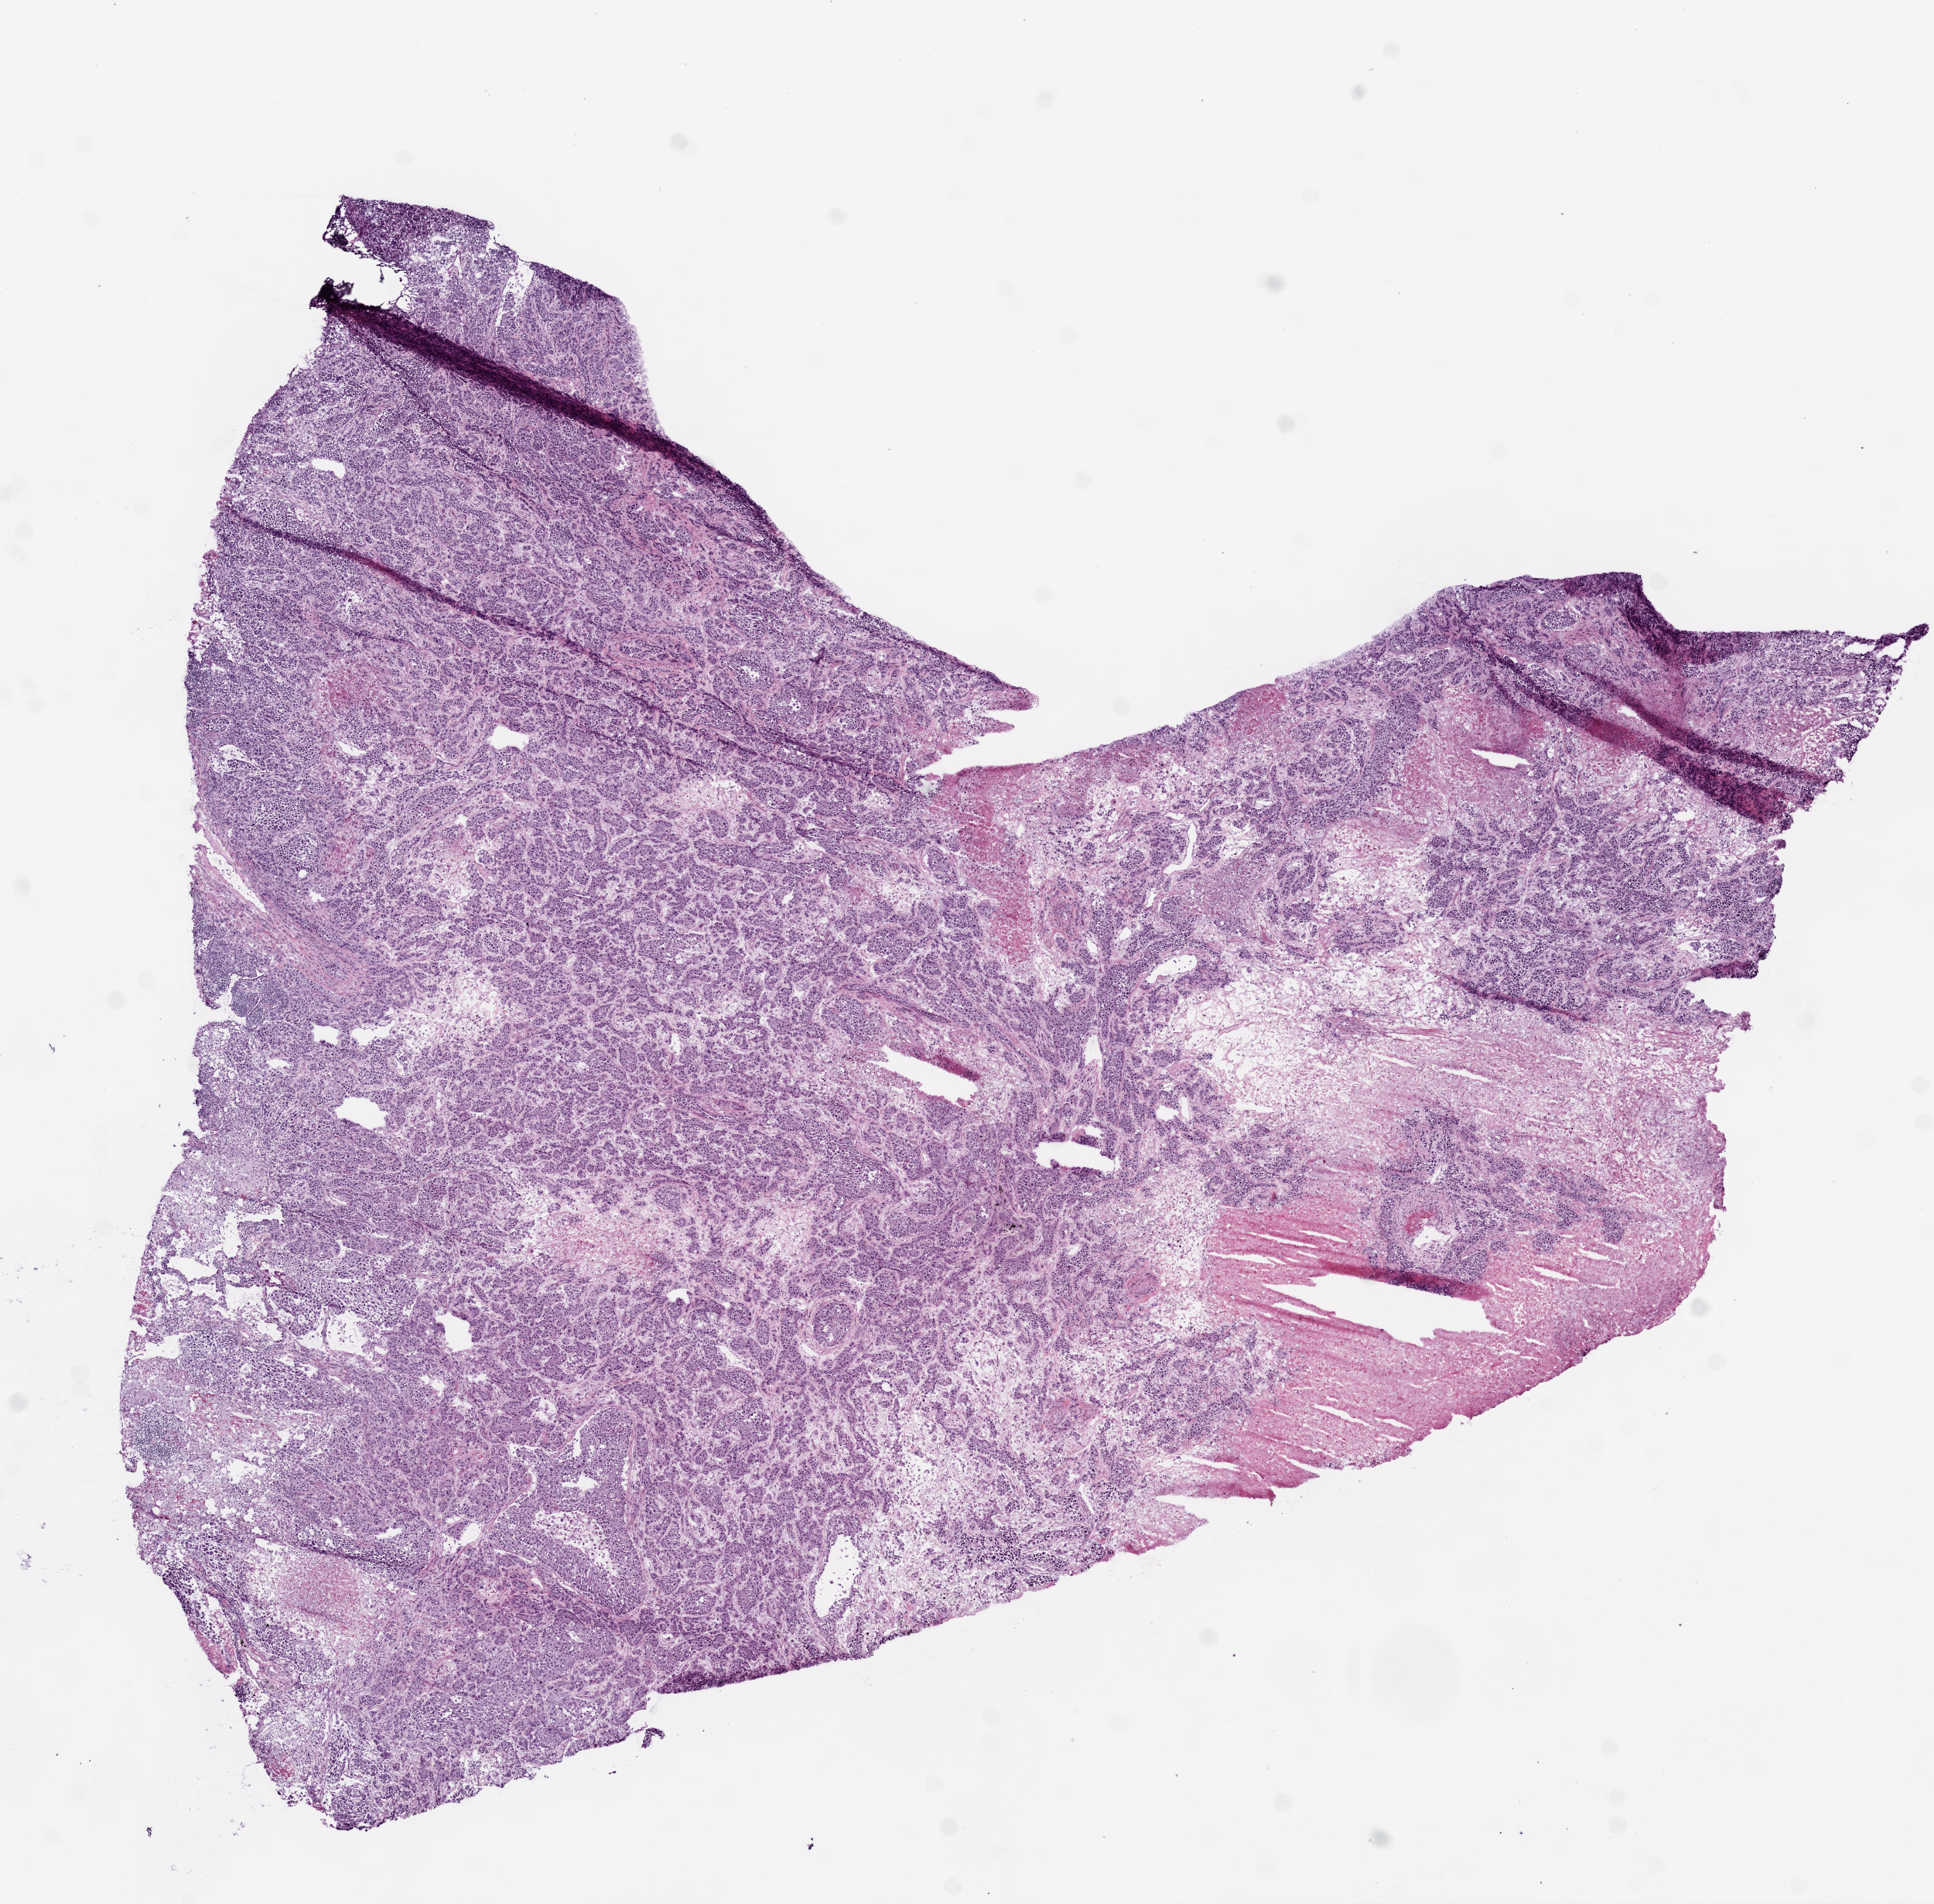
H&E-stained whole-slide image — a low-resolution overview of the entire scanned area, about 10.0 x 9.9 mm (slide scanned at 20x). Frozen section from the bottom of the tissue portion. Lung, primary tumour sample. Female patient; age at initial diagnosis 69 years. Slide review estimates, as recorded: tumour cells 90%, tumour nuclei 90%, normal cells 0%, stromal cells 0%, necrosis 10%.
• AJCC pathologic stage: IV
• histologic diagnosis: Adenocarcinoma, NOS